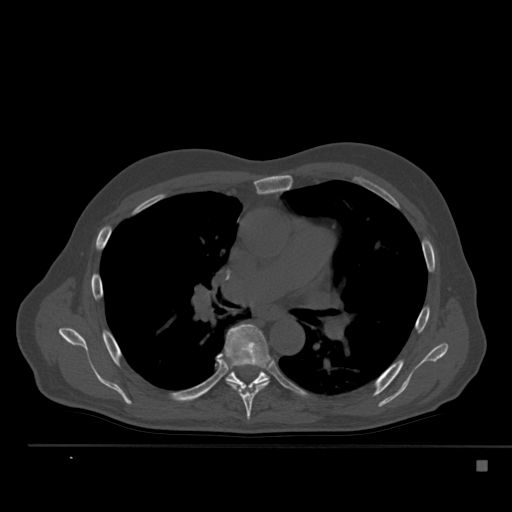
CT including the spine, one axial slice; position 339 of 517 along the scan axis; 120 kVp; bone window (W 1800 / L 400 HU); 512 × 512 image matrix. Male patient, age 70 years. From the clinical record (not read from this slice): primary cancer: renal; vertebrae with lytic lesions (as recorded): T4, T6, T10, T12, L3, L4, L5.
Annotated regions visible in this slice (semi-automatically segmented with operator editing):
- T6 vertebra: box from (x=220, y=324) to (x=270, y=420) px
- T7 vertebra: (x=226, y=365)–(x=270, y=389)